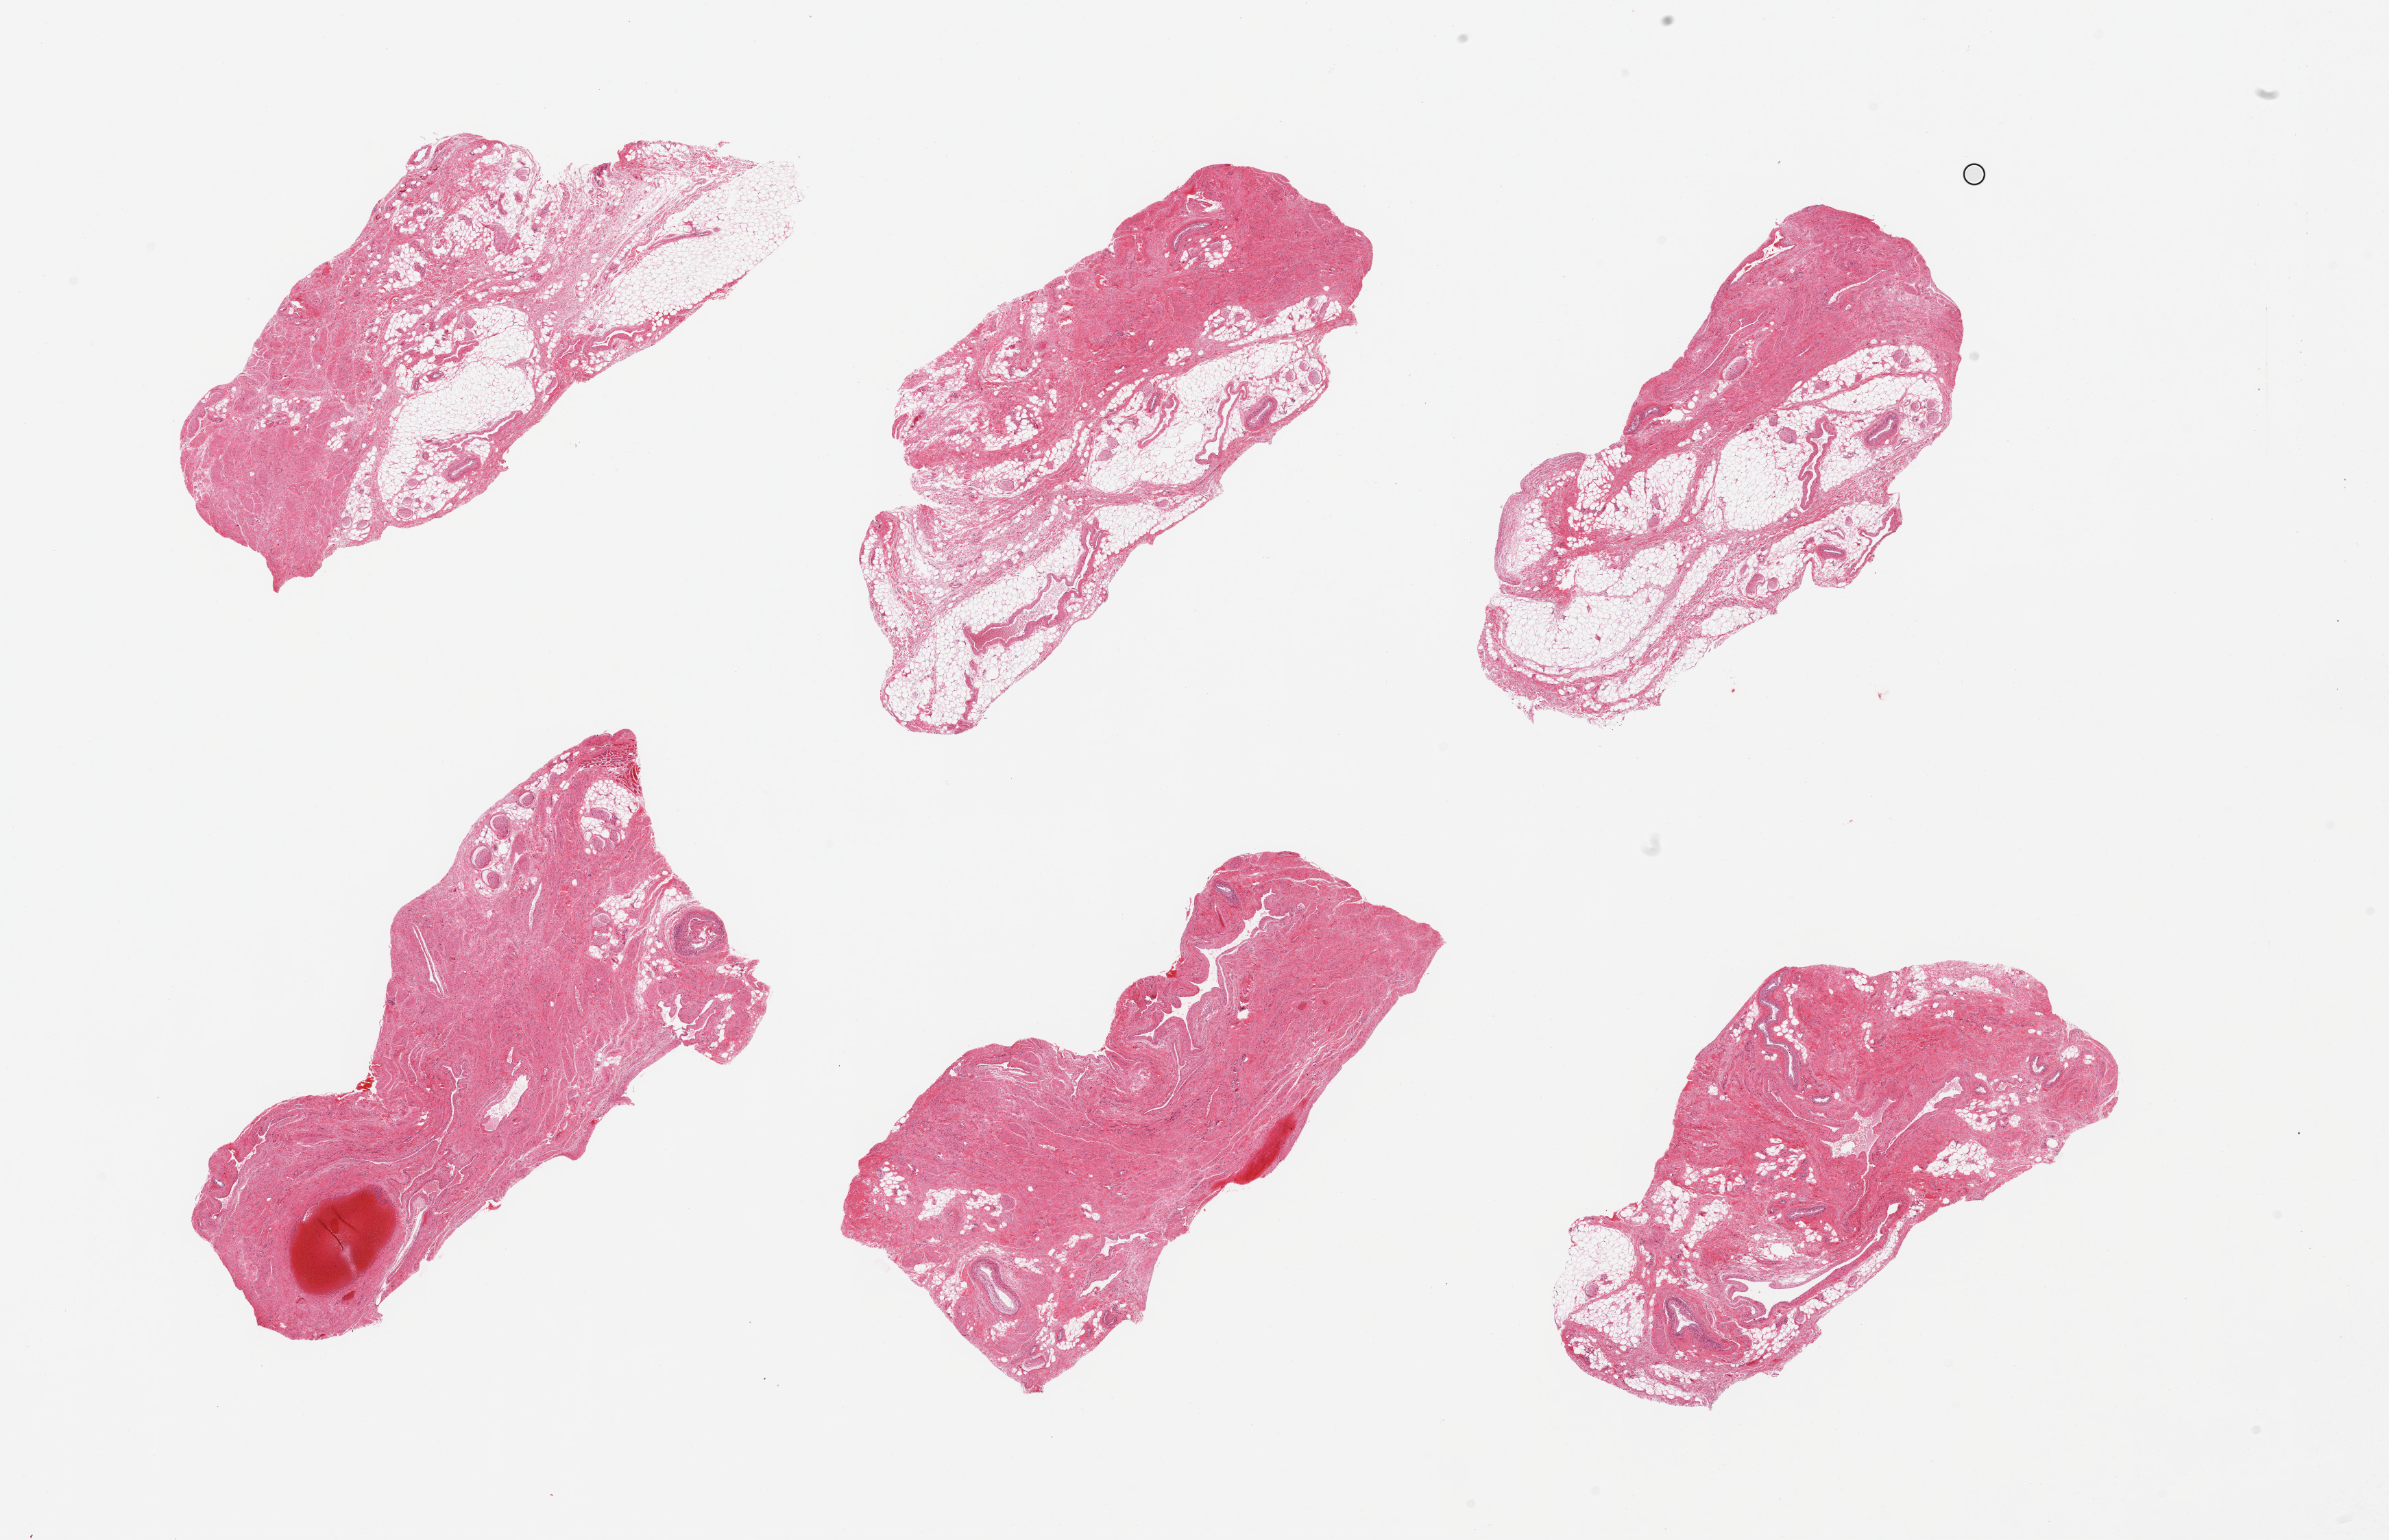
Digitized H&E-stained section, whole scanned area (about 27.6 x 17.8 mm) shown as a low-resolution overview, PAXgene-fixed paraffin-embedded (PFPE) section, sampled site (target tissue): vagina, donor tissue sample. Female donor.
Pathologist's review note for this sample: 6 pieces, fibroadipose tissue, no vaginal (squamous) mucosa.